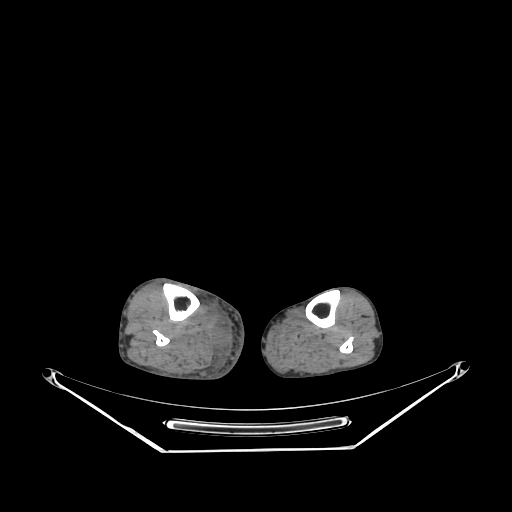
CT of an extremity soft-tissue mass (from a PET/CT study), one axial slice; position 122 of 267 along the scan axis; reconstruction kernel SOFT; 140 kVp; soft-tissue window (W 400 / L 40 HU); 3.75 mm slice thickness; 512 × 512 image matrix. Male patient. From the clinical record (not read from this slice): histological type: pleiomorphic liposarcoma; grade: high; site of the primary tumour: right calf.
Structures marked on this image (expert contour drawn on MRI and transferred to this co-registered scan by the dataset authors):
- gross tumour volume including surrounding oedema: bounding box (x1, y1, x2, y2) in pixels: (210, 329, 225, 350)